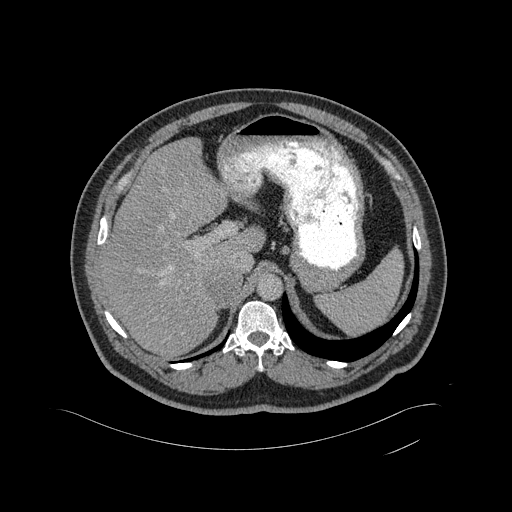
Contrast-enhanced abdominal CT, one axial slice. Slice 336 of 433 in the series (ordered by position). Soft-tissue window (W 400 / L 40 HU). 512 × 512 image matrix. Patient: male, 56 years. From the clinical record (not read from this slice): diagnosis: adrenocortical carcinoma; tumour side: right adrenal; tumour size at pathology: 11.6 cm; Ki-67 index: 50 %; stage (as recorded): 3.
Annotated regions visible in this slice (semi-automatic segmentation, software-assisted and operator-edited):
- mass: bounding box <207,269,240,302> (left, top, right, bottom; pixels)